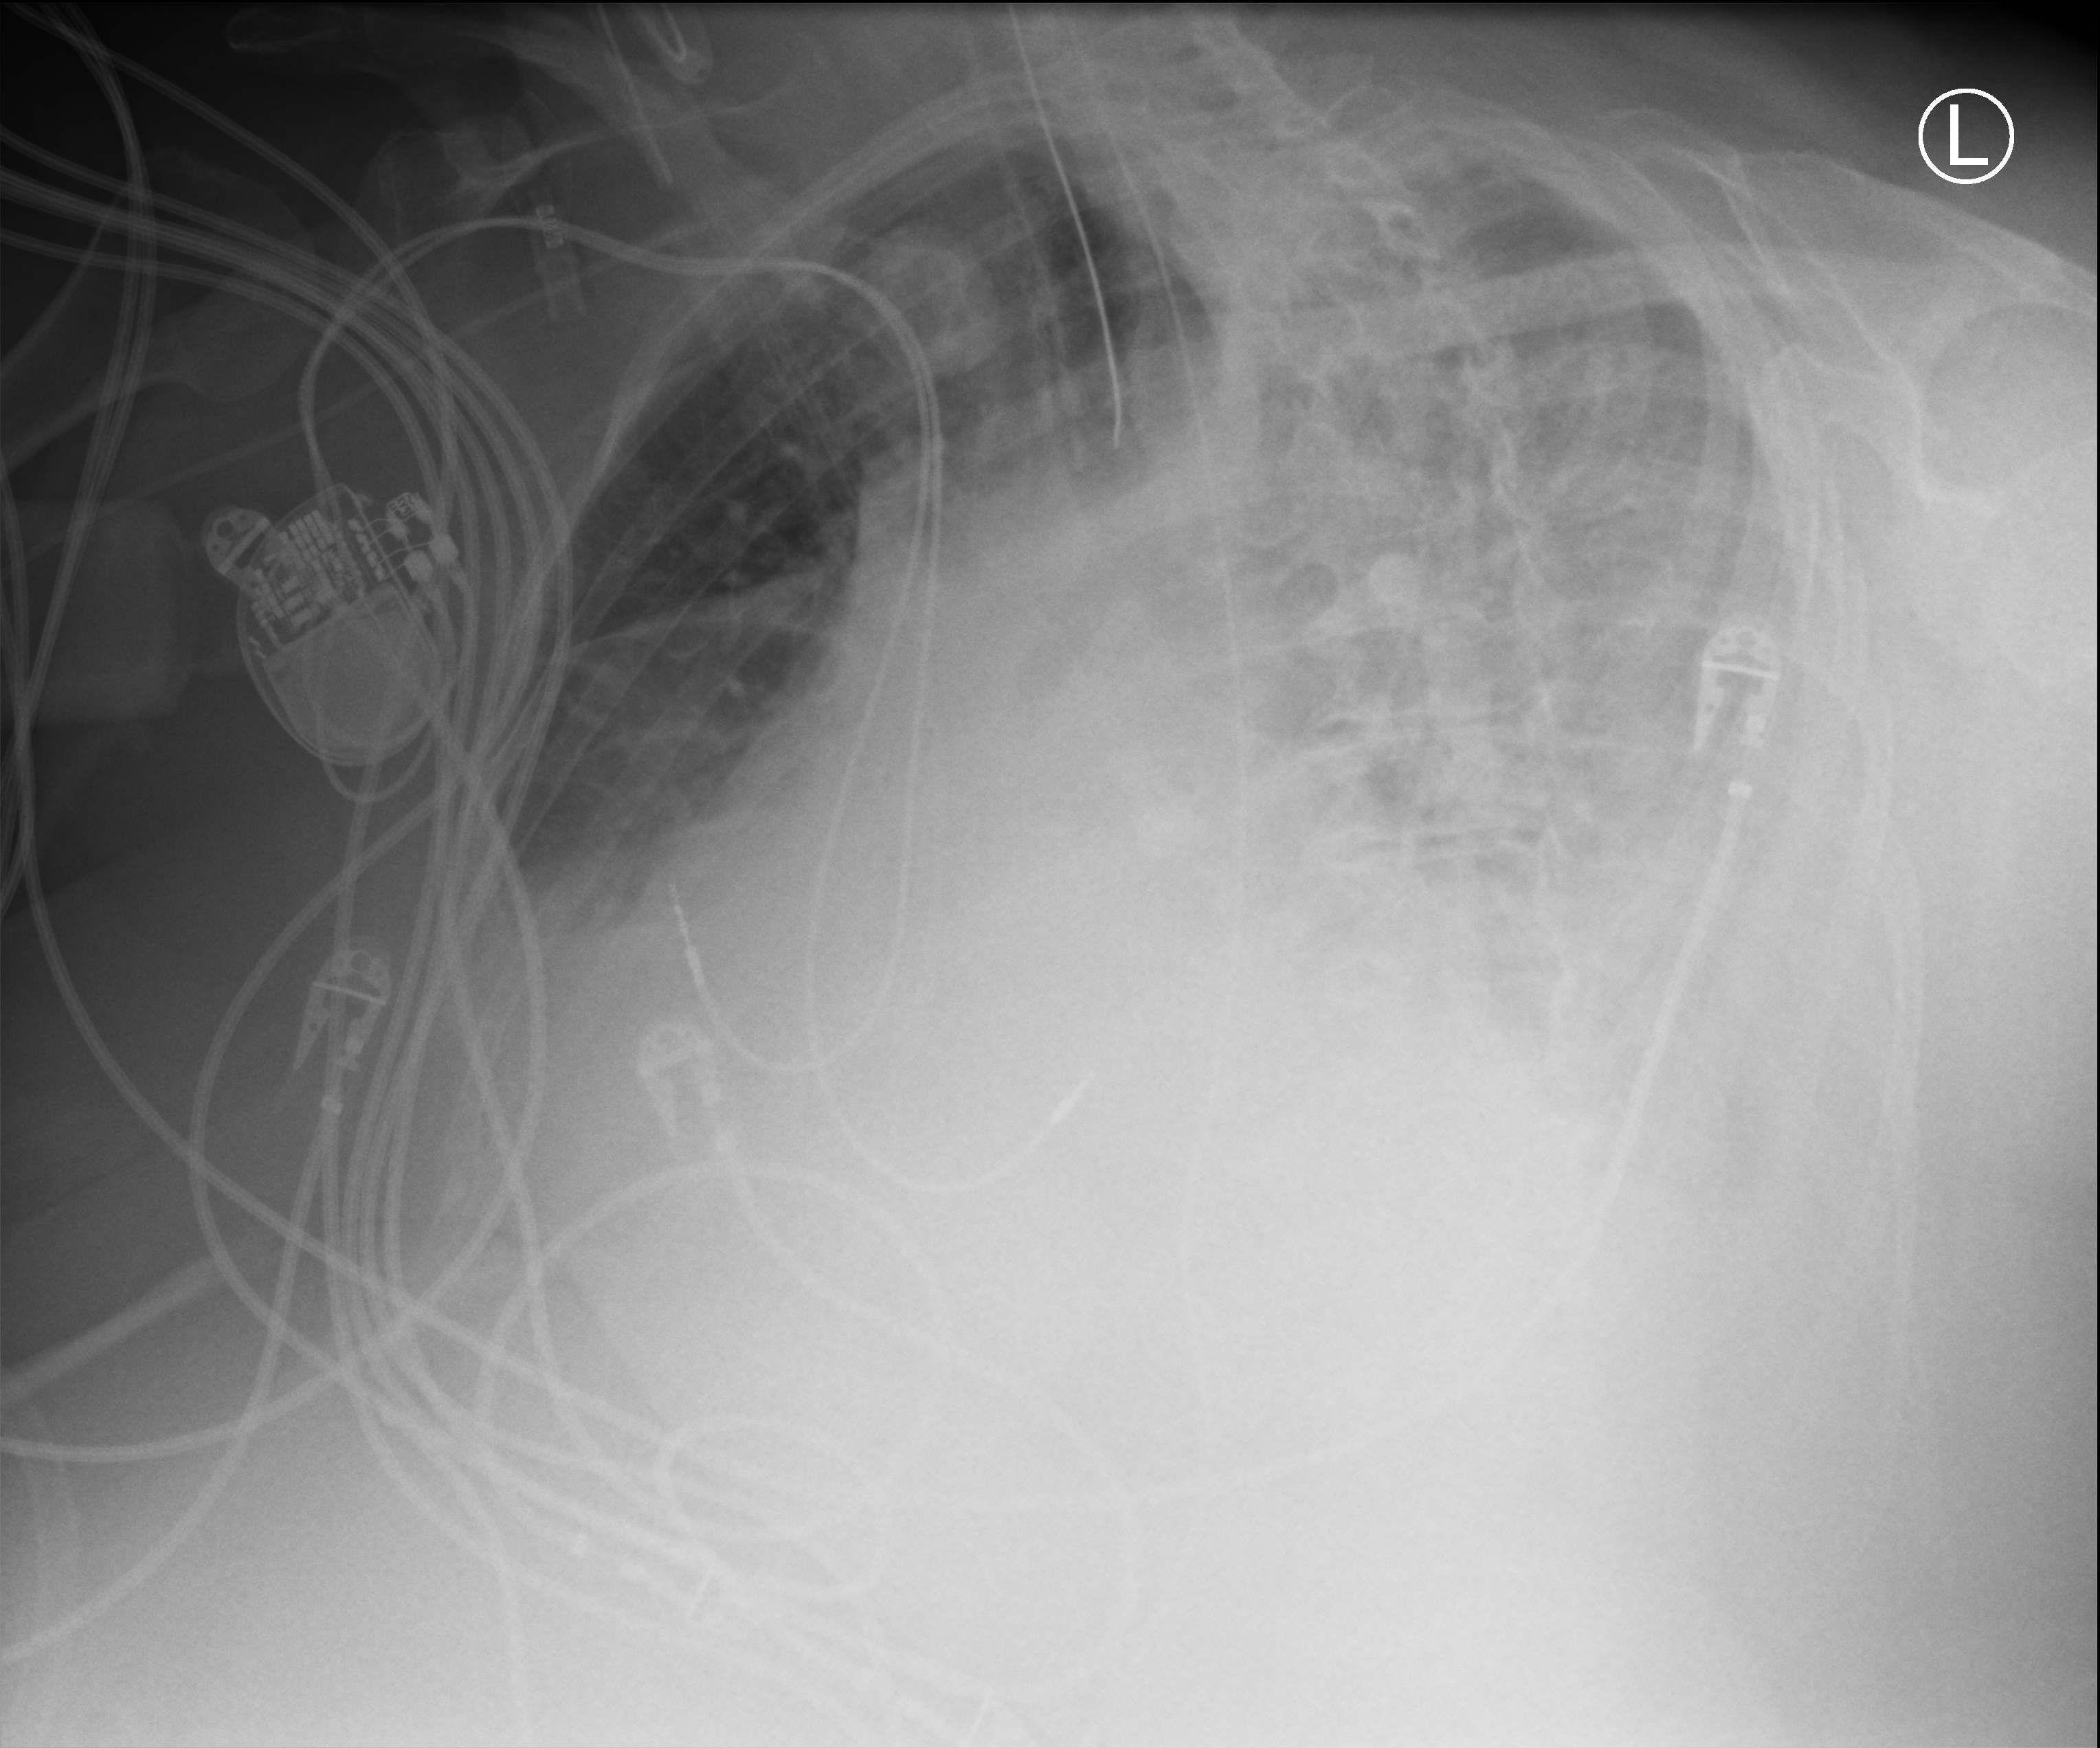
Portable chest radiograph. Patient hospitalised with COVID-19; female, aged 75–90 years.
Admission-level facts for this patient (not findings on this image; timing relative to this image not recorded):
- admitted to intensive care during this hospital stay: yes